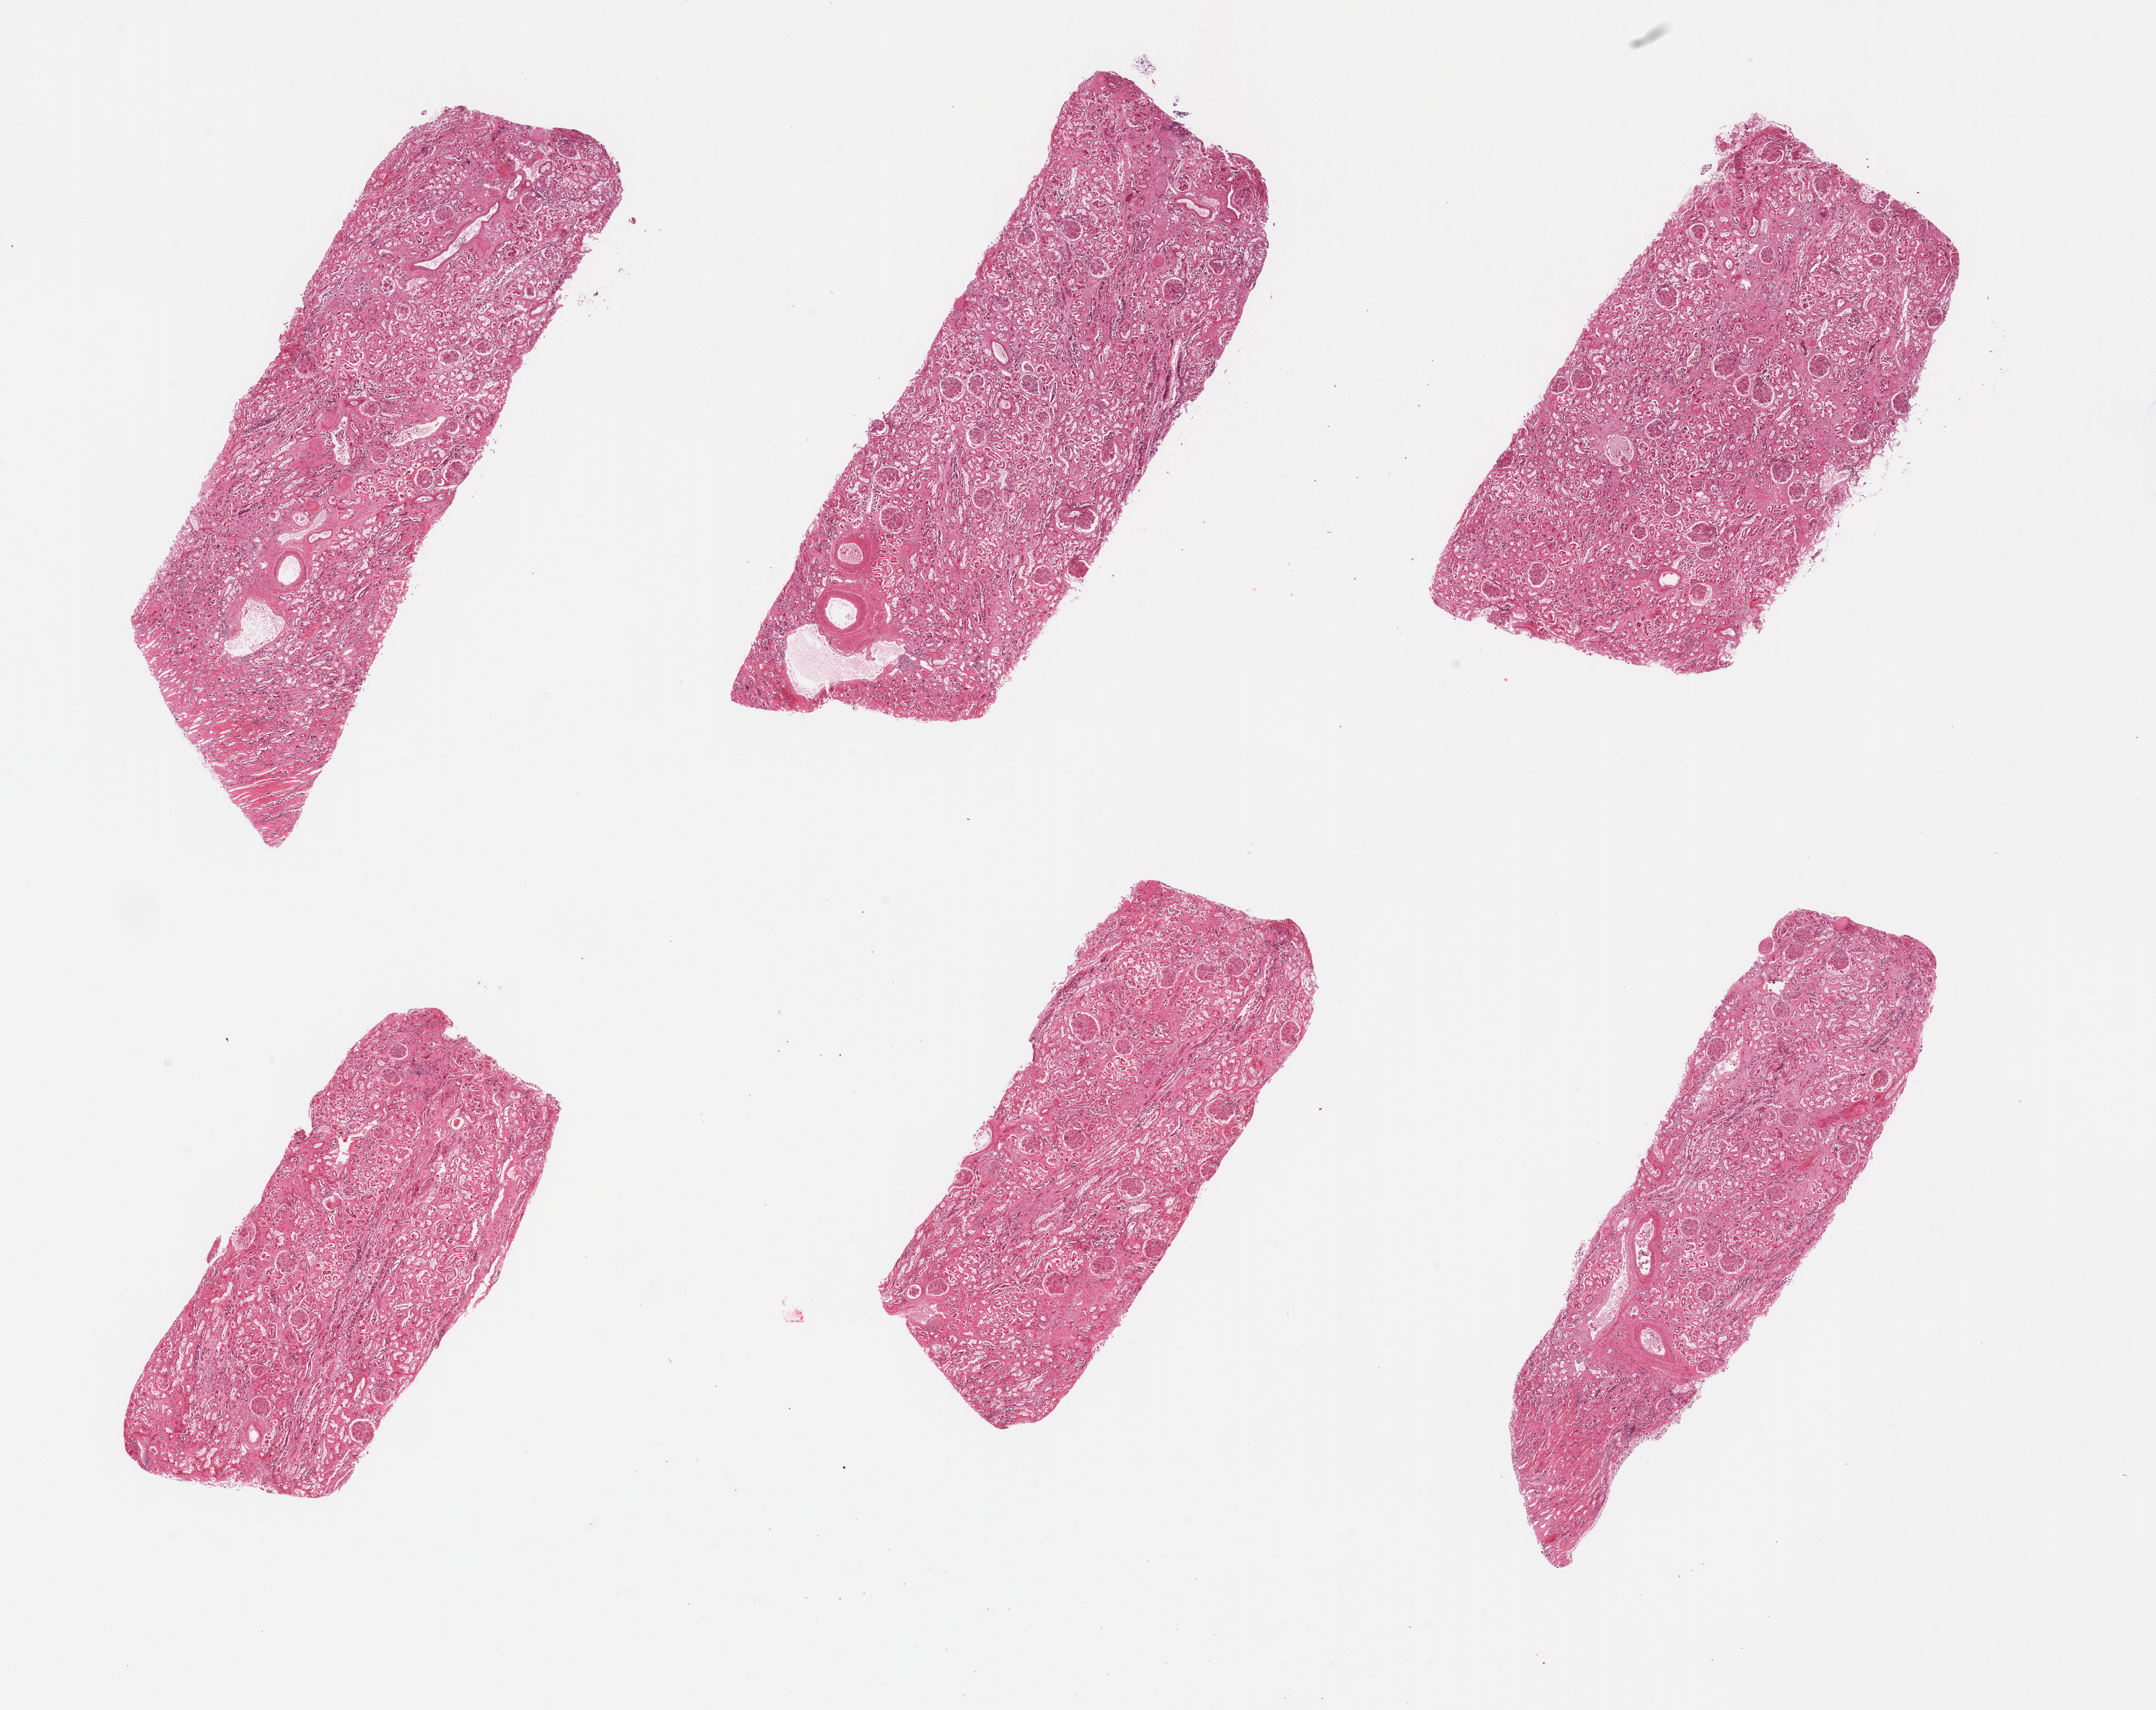
Haematoxylin and eosin whole-slide image — a low-resolution overview of the entire scanned area, about 23.6 x 18.7 mm, PAXgene-fixed, paraffin-embedded tissue, section of renal cortex (target tissue), donor tissue sample. Male donor.
• review note (as recorded): 6 pieces; moderate interstitial fibrosis; tubules severely autolyzed, glomeruli in relatively good shape